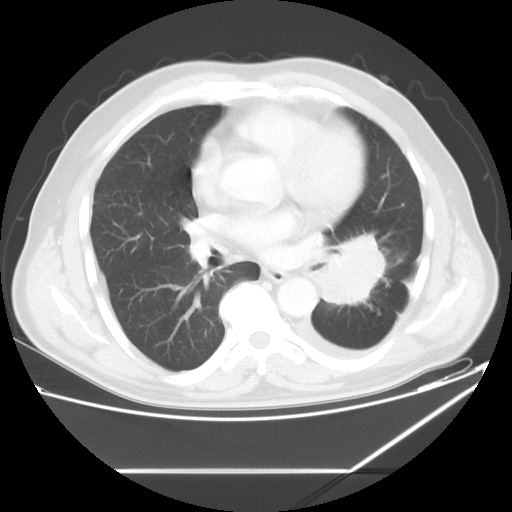
Chest CT, one axial slice. Position 30 of 60 along the scan axis. Reconstruction kernel STANDARD. Lung window (W 1500 / L -600 HU). 5 mm slice thickness. 512 × 512 image matrix. Patient: male, 62 years. From the clinical record (not read from this slice): clinical TNM (as recorded): T3 N0 M1.
Structures marked on this image (rectangle marked by the reading radiologist):
- lung tumour (recorded histology: adenocarcinoma): bounding box (x1, y1, x2, y2) in pixels: (312, 230, 387, 311)
- lung tumour (recorded histology: adenocarcinoma): (316, 233, 382, 308)